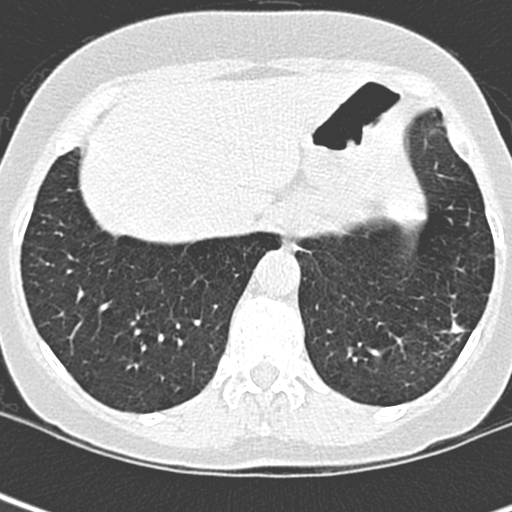
Low-dose screening chest CT, one axial slice; position 61 of 252 along the scan axis; lung window (W 1500 / L -600 HU); 1.3 mm slice thickness; 512 × 512 image matrix.
Structures marked on this image (manually delineated by an expert):
- lesion 1 (tumor, lower lobe of left lung): bounding box (x1, y1, x2, y2) in pixels: (449, 320, 466, 334)